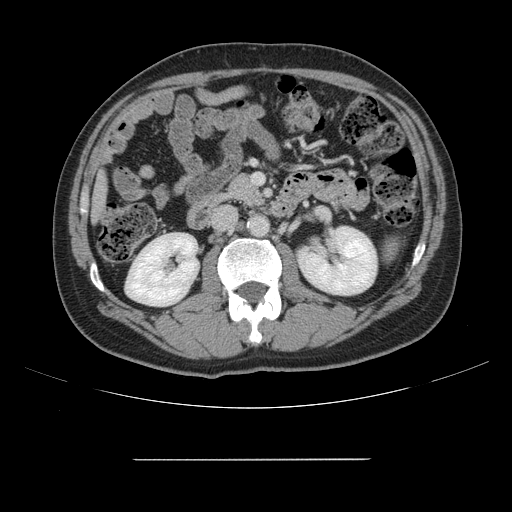
Contrast-enhanced abdominal CT, one axial slice; slice 53 of 164 in the series (ordered by position); 120 kVp; intravenous contrast given; soft-tissue window (W 400 / L 40 HU); 2.5 mm slice thickness; 512 × 512 image matrix, field of view 404 × 404 mm. Male patient, age 54 years. Case-level facts recorded for this patient, not image findings: diagnosis: colorectal cancer liver metastases, imaged before liver resection; multiple liver metastases: yes.
Outlined on this slice (expert manual segmentation):
- liver: bounding box [x1, y1, x2, y2] px = [94, 179, 105, 216]
- planned liver remnant (the part of the liver to remain after resection): [93, 180, 105, 217]